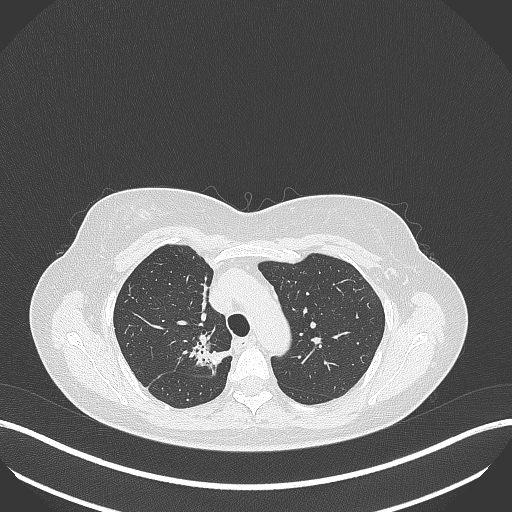
Chest CT, one axial slice; position 291 of 386 along the scan axis; 120 kVp; lung window (W 1500 / L -600 HU); 512 × 512 image matrix, field of view 400 × 400 mm. Patient: female, 65 years. From the clinical record (not read from this slice): clinical TNM (as recorded): T1b N0 M0; histopathological grade: G2.
Annotated regions visible in this slice (rectangle marked by the reading radiologist):
- lung tumour (recorded histology: adenocarcinoma): bounding box [x1, y1, x2, y2] px = [191, 339, 229, 374]